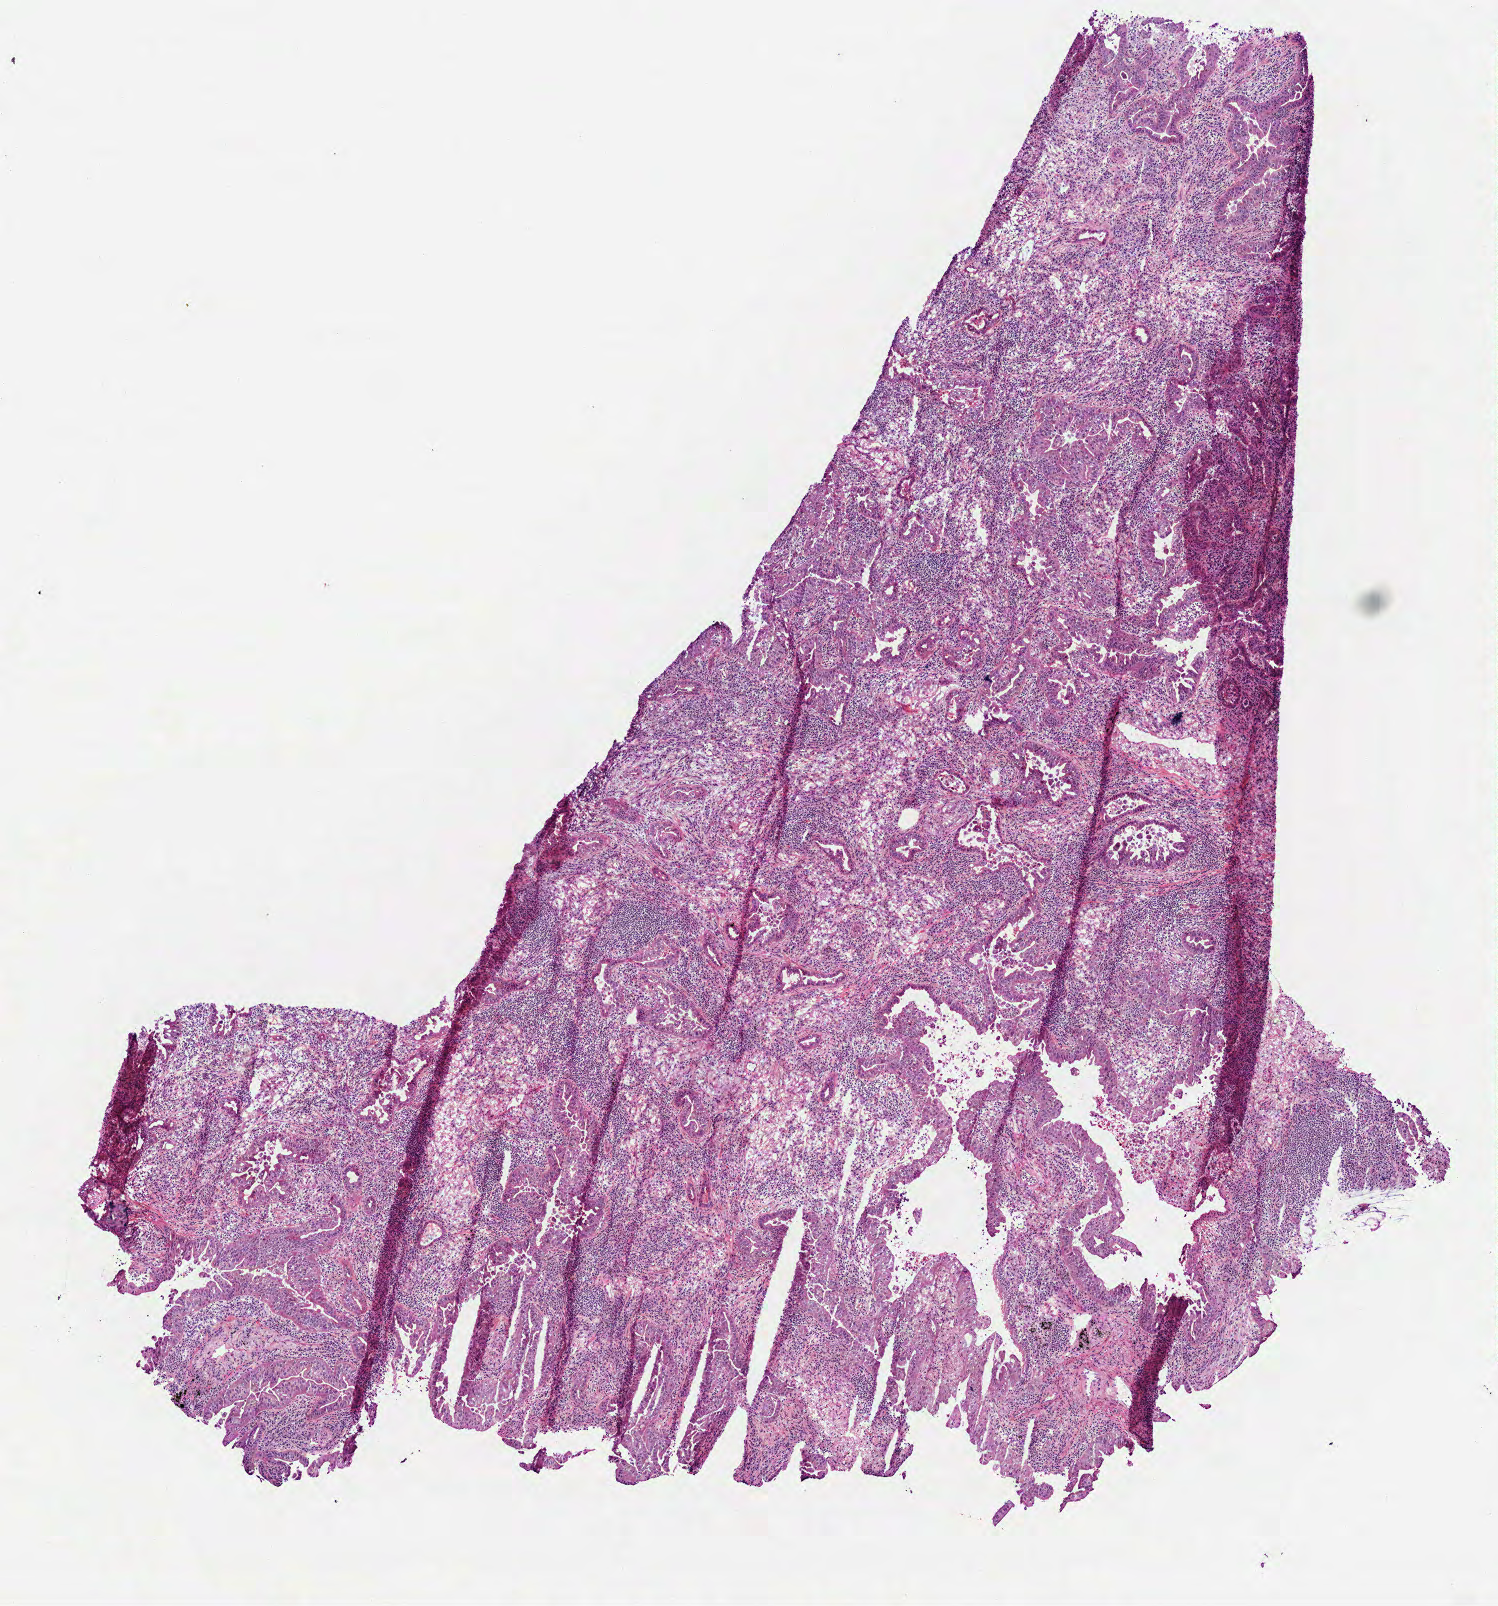
H&E-stained whole-slide image, whole scanned area (about 6.0 x 6.5 mm, from a 40x scan) shown as a low-resolution overview; frozen section from the bottom of the tissue portion; primary tumour sample from the lung. Male patient; age at initial diagnosis 84 years. Slide review estimates, as recorded: tumour cells 75%, tumour nuclei 50%.
Diagnosis: Acinar cell carcinoma (lower lobe, lung).